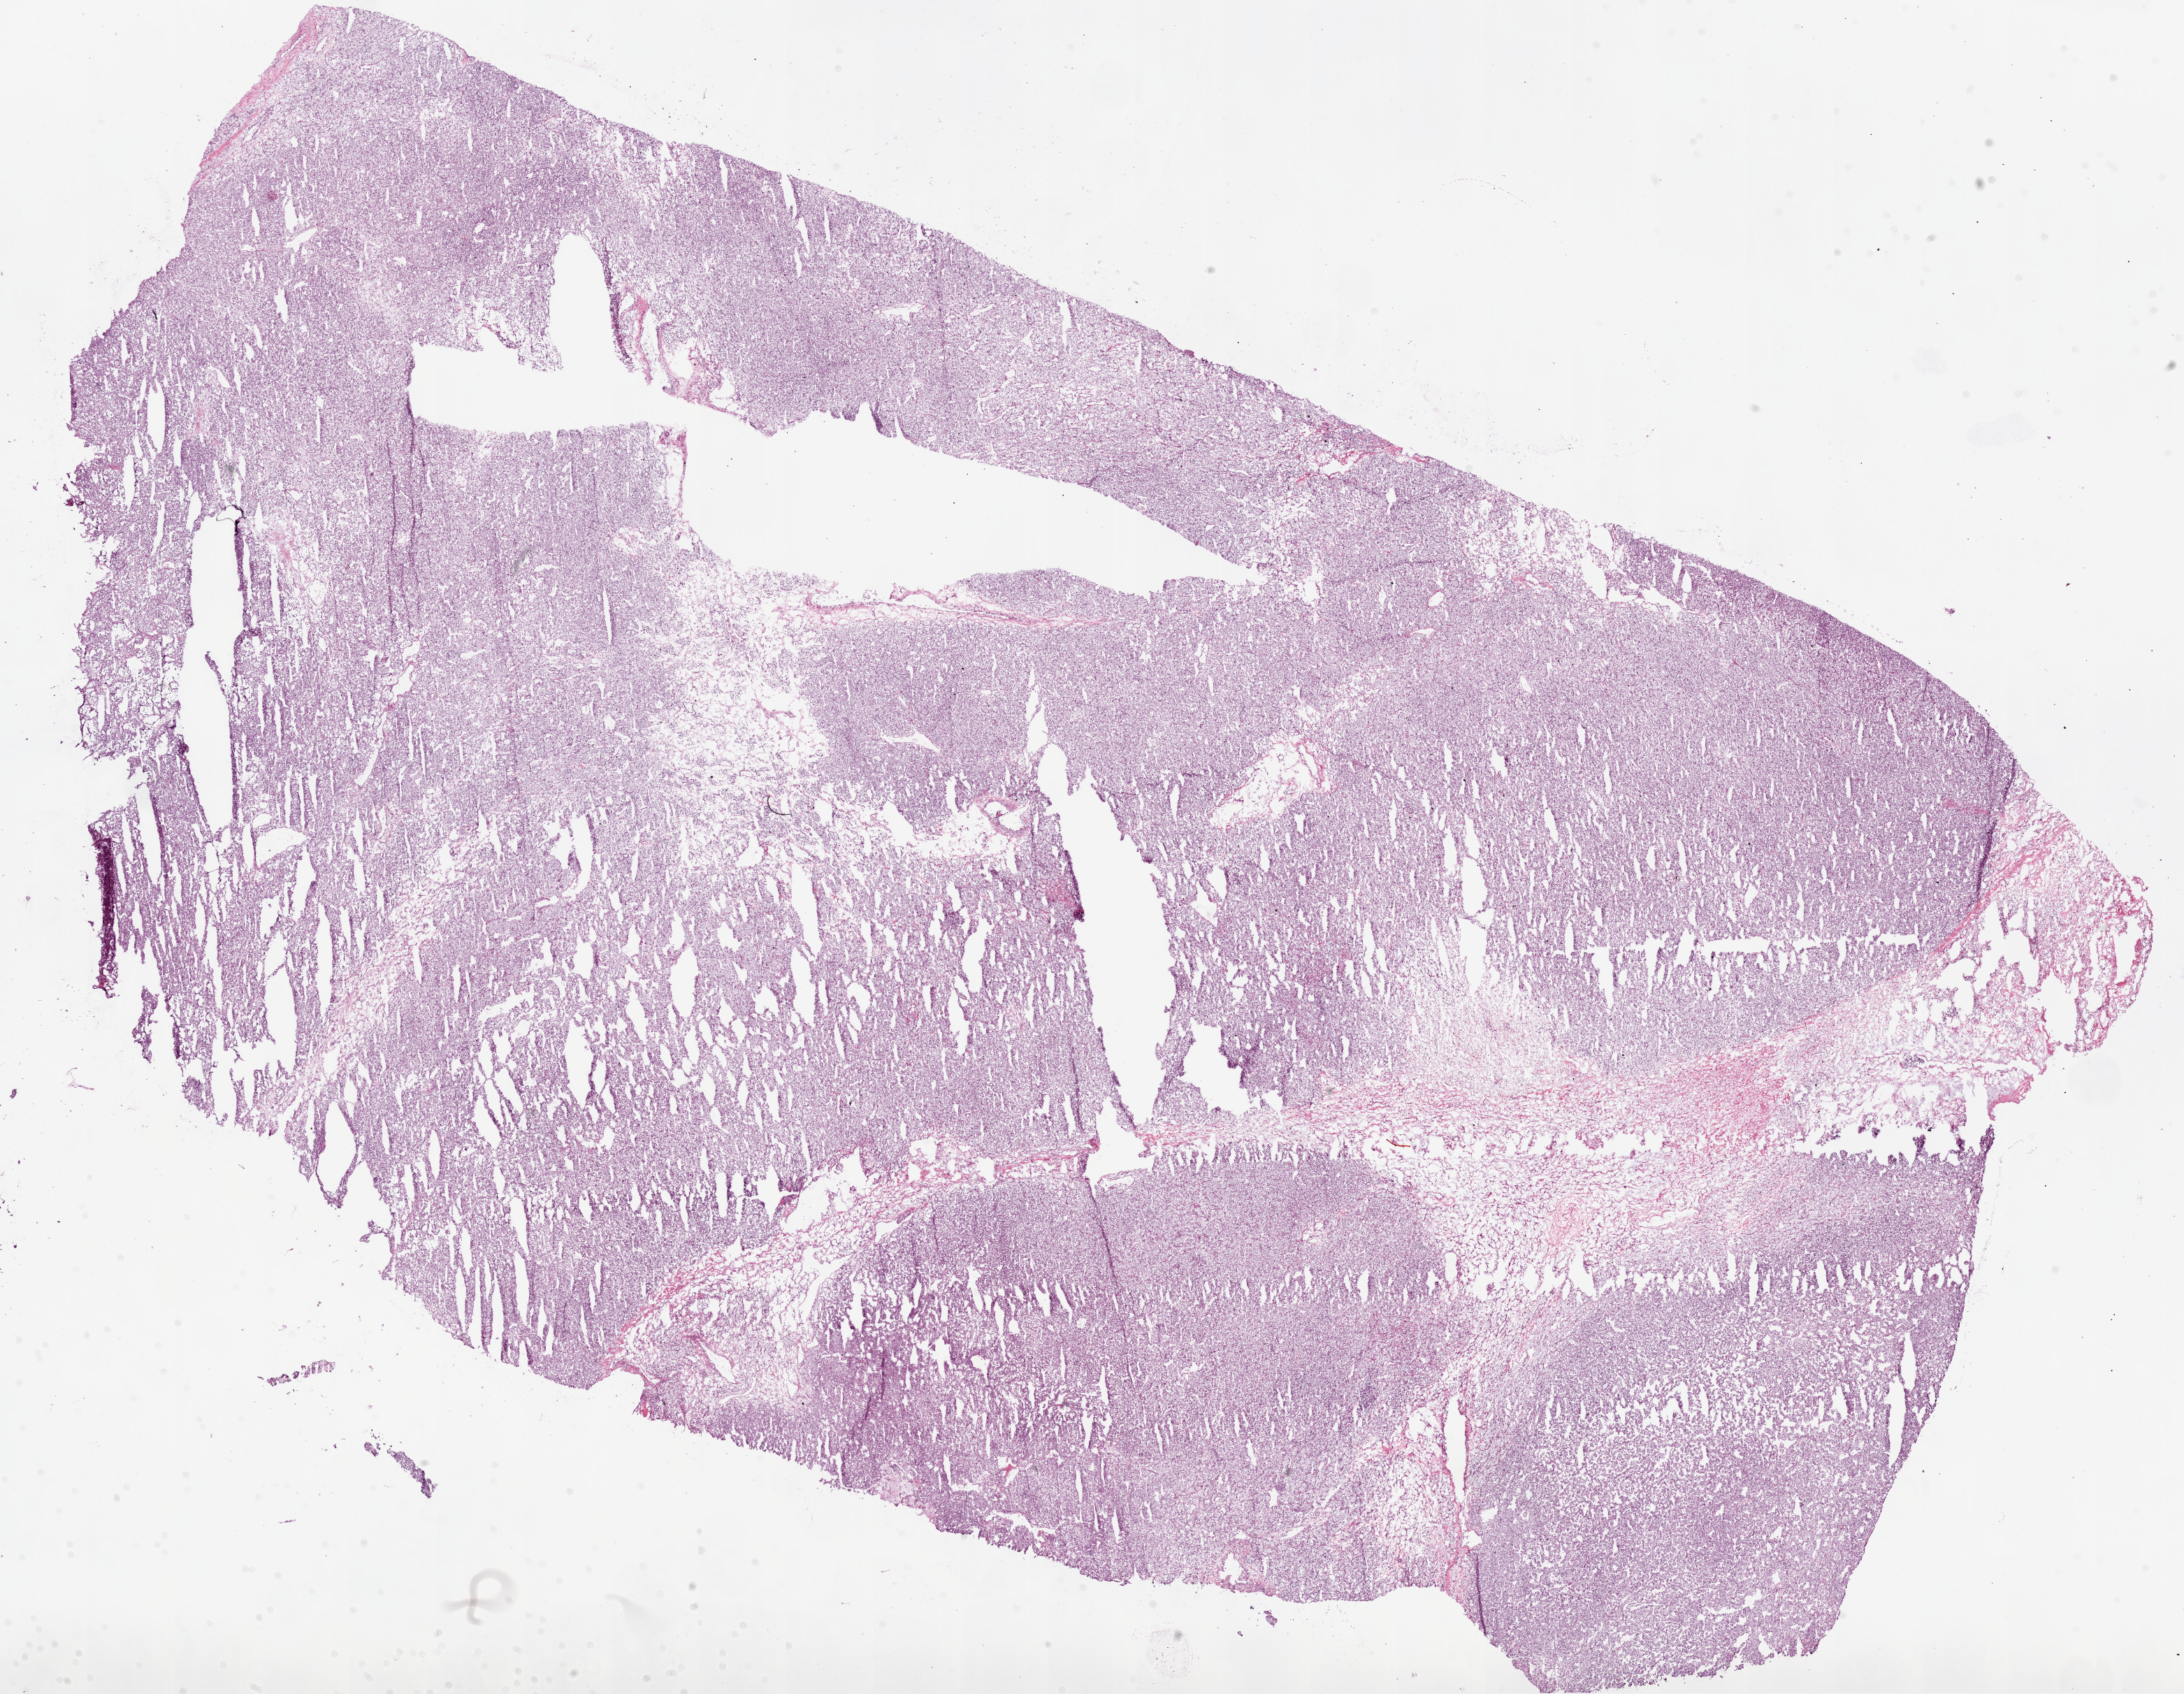
H&E whole-slide image, a low-resolution overview of the entire scanned area, about 25.1 x 19.5 mm. Frozen section from the bottom of the tissue portion. Primary tumour sample from the kidney. Patient: male, age at initial diagnosis 50 years. Histologic grade: G3 (poorly differentiated). Pathologist review of this section (percent, as recorded): tumour cells 82%, tumour nuclei 85%, normal cells 0%, stromal cells 18%, necrosis 0%.
* TNM: T3b NX M0
* pathologic diagnosis: Clear cell adenocarcinoma, NOS
* AJCC pathologic stage: III